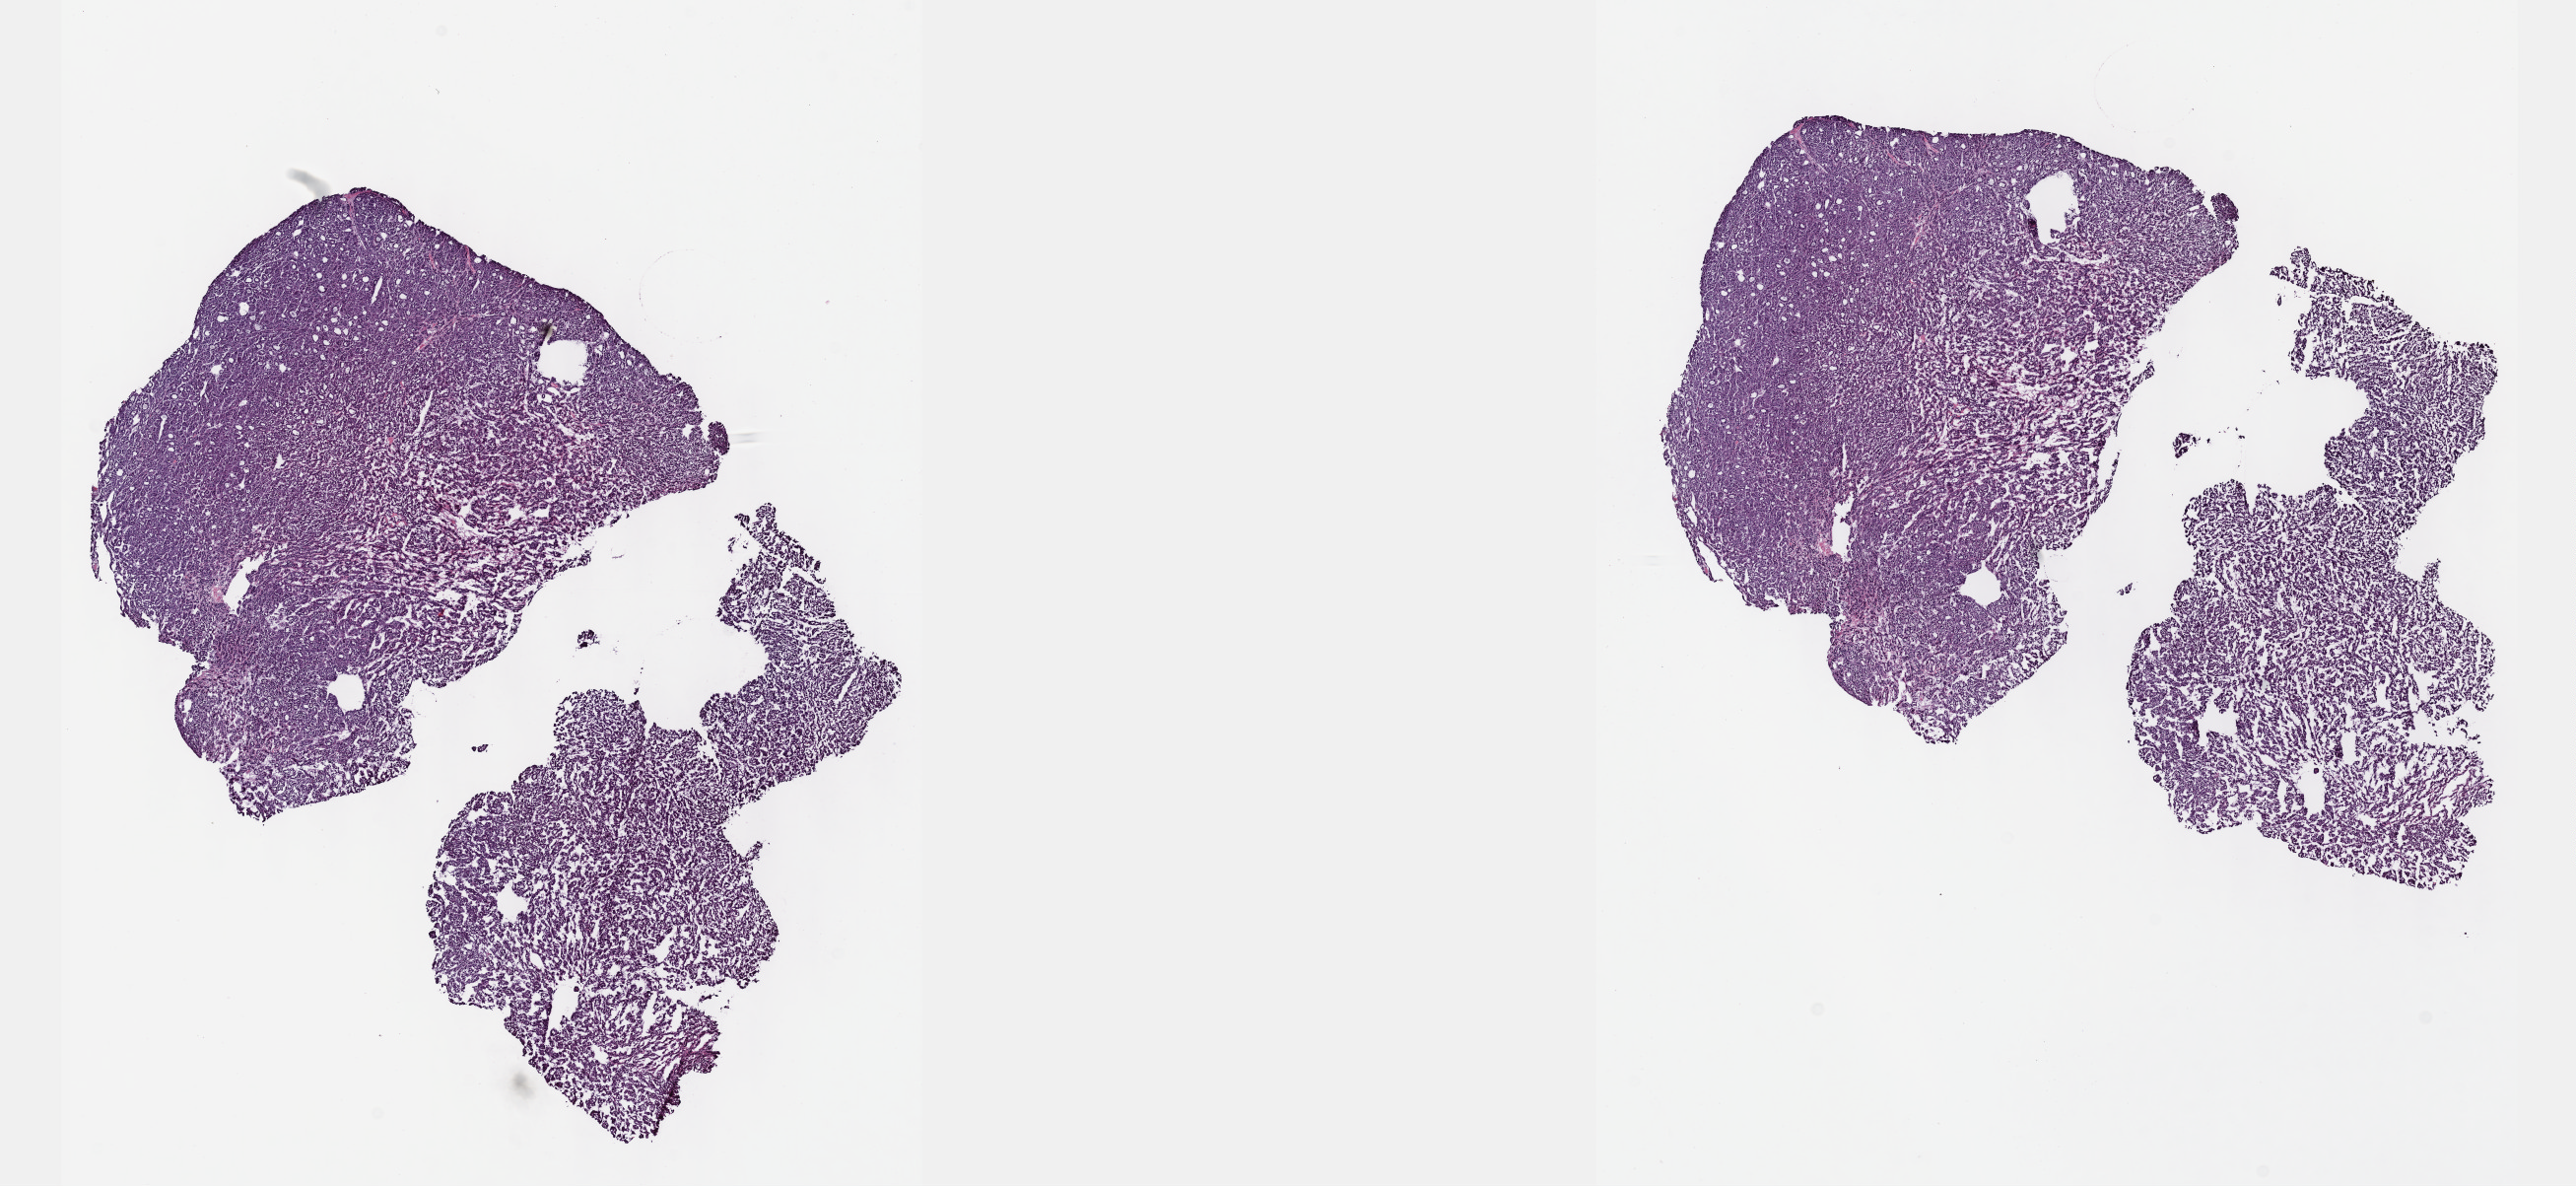
Whole-slide histology image, H&E-stained — low-resolution overview of the scanned area, about 21.1 x 9.7 mm (acquisition: 40x scan). Frozen section from the top of the tissue portion. Sample: primary tumour, liver. Male, age 69 years at initial diagnosis. Histologic grade: G2 (moderately differentiated). Slide review estimates, as recorded: tumour cells 85%, tumour nuclei 85%, normal cells 0%, stromal cells 15%, necrosis 0%. Inflammatory infiltration, as recorded: lymphocyte infiltration 2%, monocyte infiltration 1%, neutrophil infiltration 3%.
AJCC pathologic stage: I. Diagnosis: Hepatocellular carcinoma, NOS.